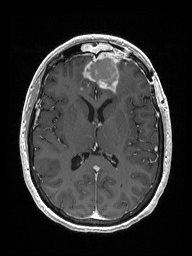
Brain MRI from a brain-tumour surgery series, one axial slice. Slice 80 of 192 in the series (ordered by position). T1-weighted post-contrast. 1 mm slice thickness. 192 × 256 image matrix, field of view 187 × 250 mm. Case-level facts recorded for this patient, not image findings: histopathology: Metastastic Carcinoma from Breast primary; tumour location: Right Frontal.
Outlined on this slice (expert manual segmentation):
- previous resection cavity: box from (x=85, y=52) to (x=119, y=86) px